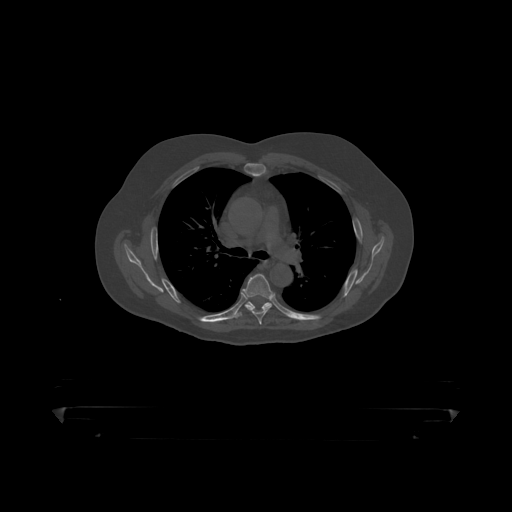
CT including the spine, one axial slice; slice 313 of 390 in the series (ordered by position); reconstruction kernel STANDARD; 120 kVp; bone window (W 1800 / L 400 HU); 1.25 mm slice thickness; 512 × 512 image matrix, field of view 650 × 650 mm. Patient: male, 60 years. Case-level facts recorded for this patient, not image findings: primary cancer: prostate.
Outlined on this slice (semi-automatically segmented with operator editing):
- T5 vertebra: bounding box [x1, y1, x2, y2] px = [242, 274, 275, 319]
- T6 vertebra: [235, 301, 272, 317]